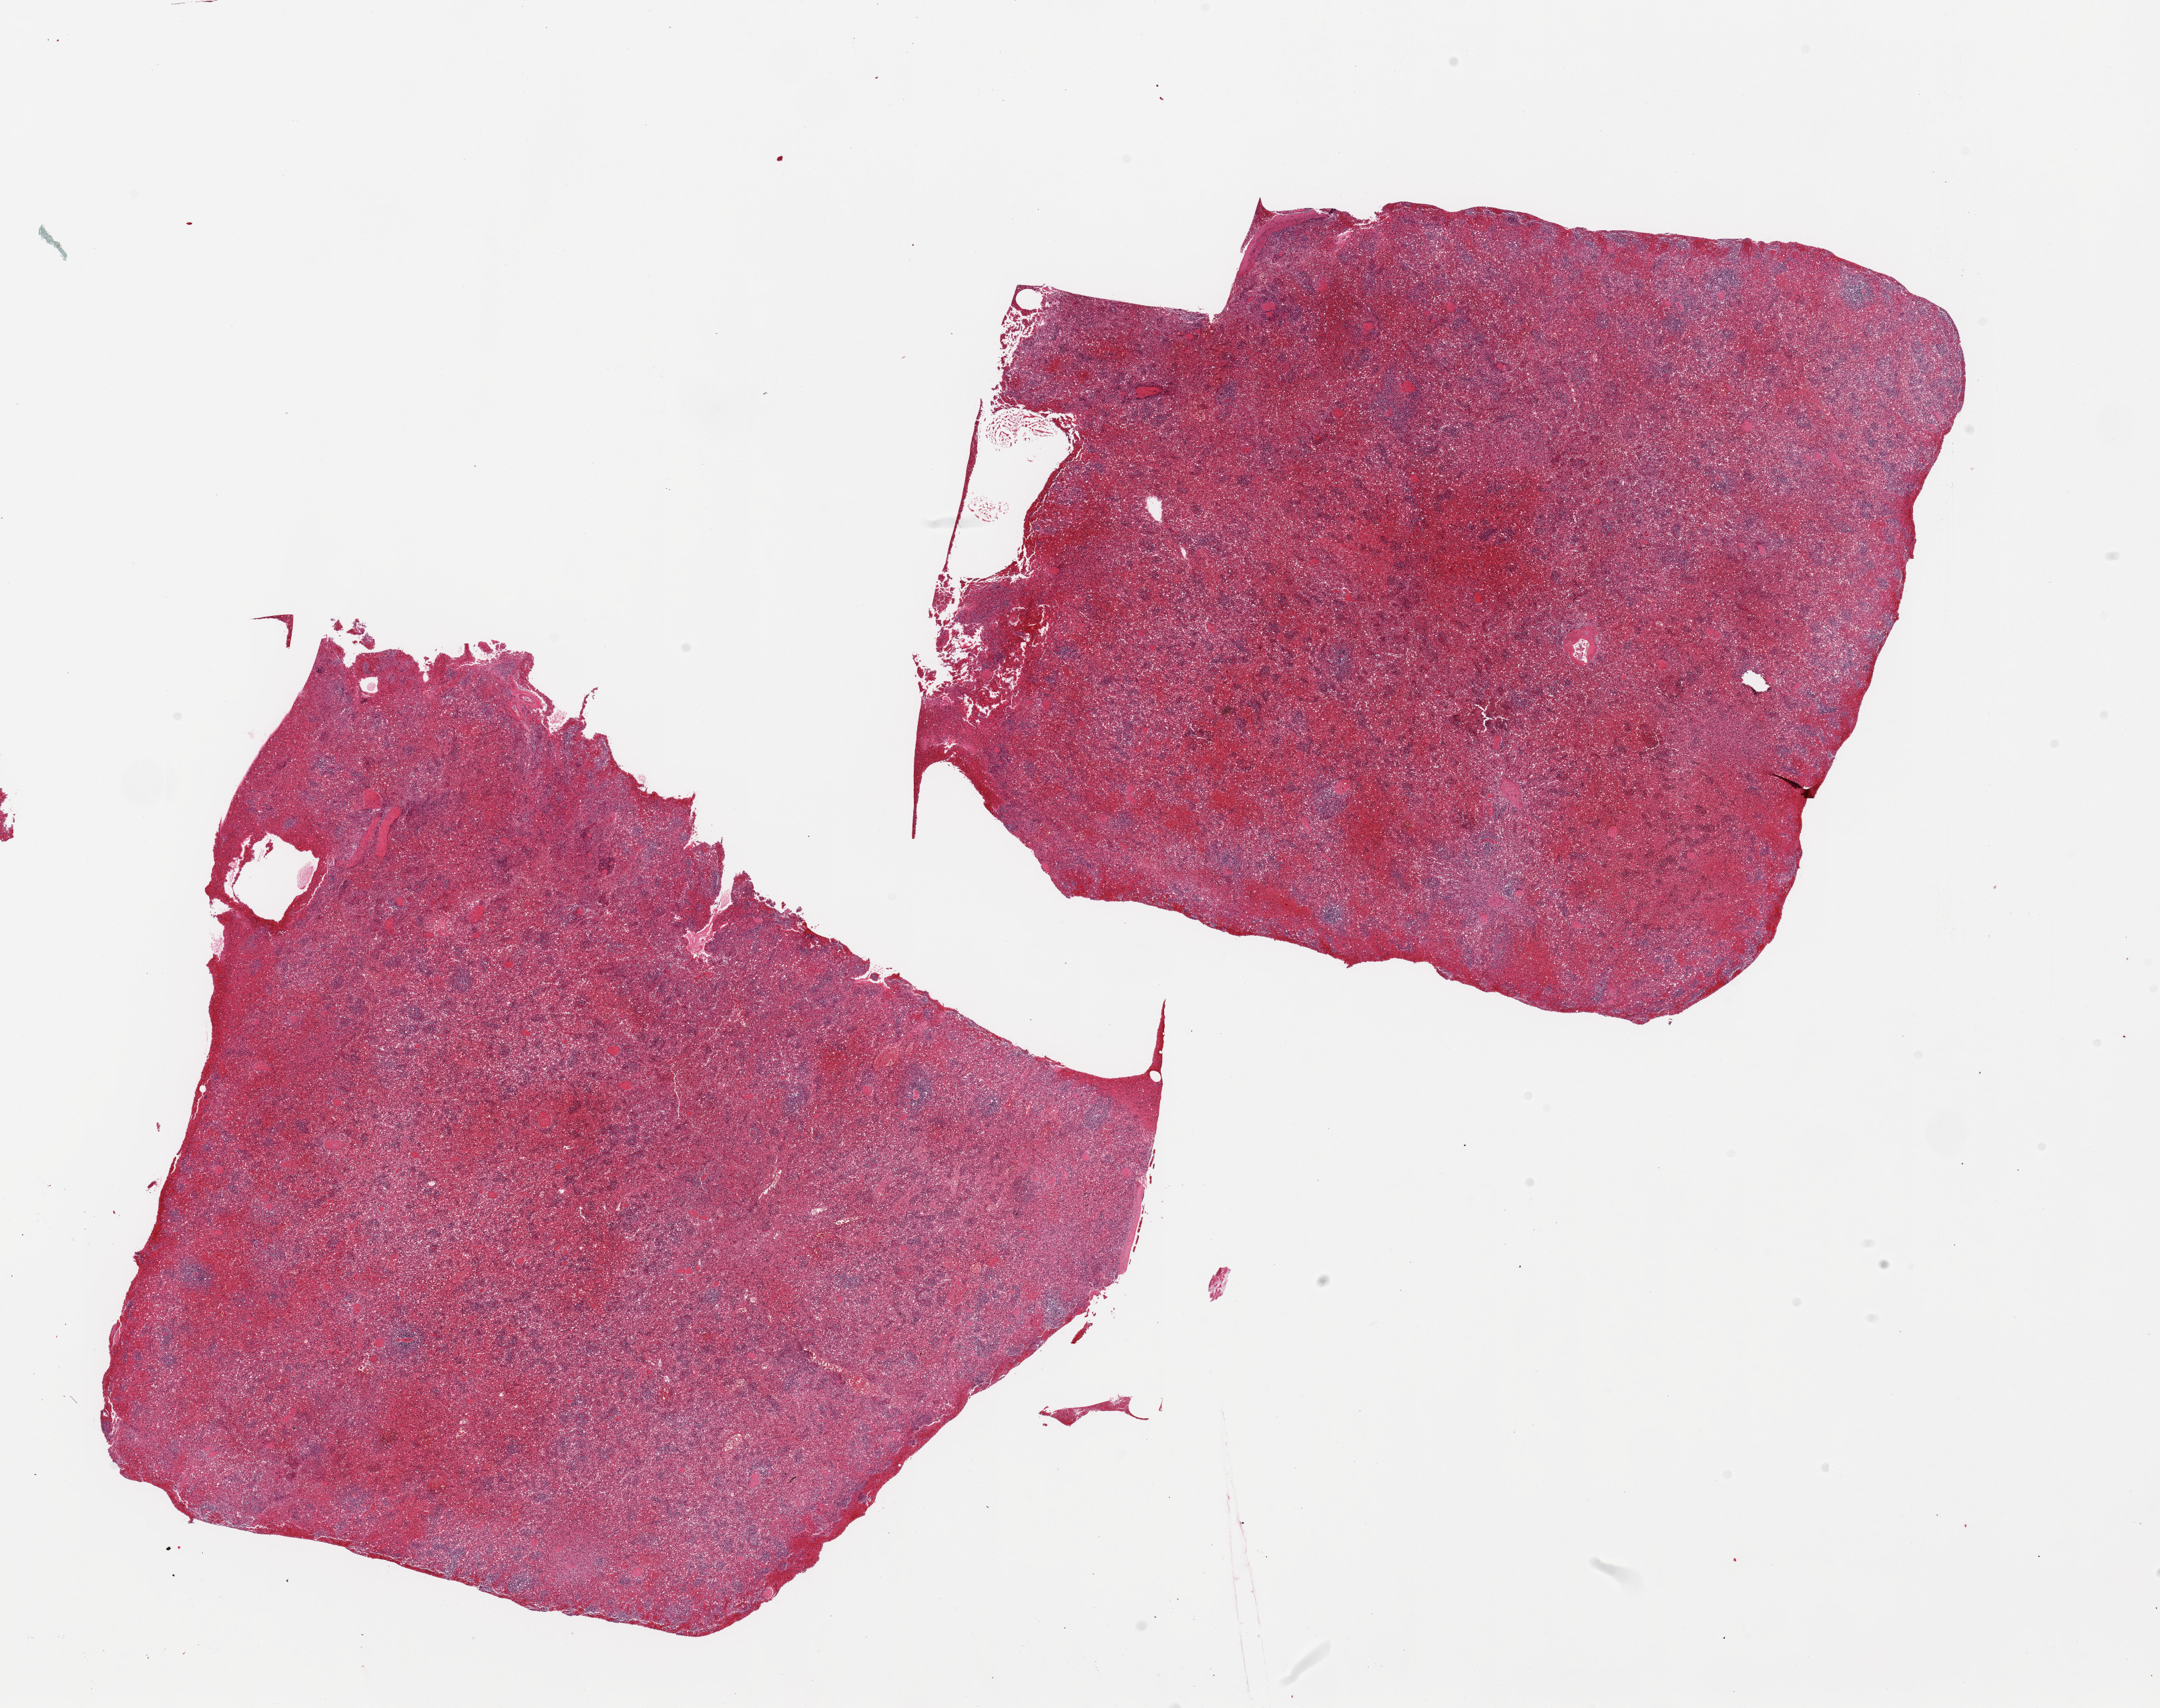
Haematoxylin and eosin whole-slide image — shown as a low-resolution overview of the whole scanned area (about 25.6 x 20.2 mm, from a 20x scan); PAXgene-fixed, paraffin-embedded tissue; target tissue: spleen; donor tissue sample.
* pathologist's review note for this sample: 2 pieces; focally congested